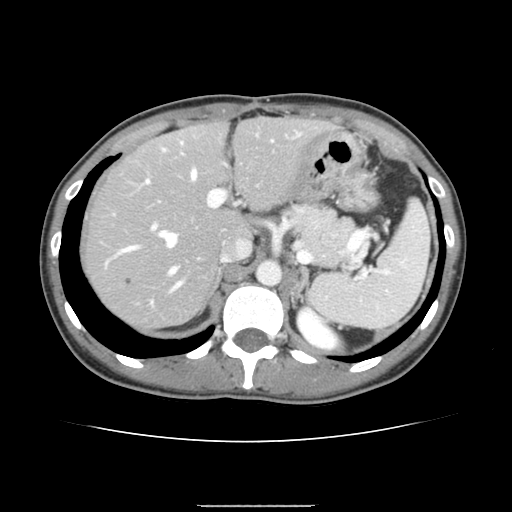
Contrast-enhanced abdominal CT, one axial slice; position 103 of 150 along the scan axis; intravenous contrast given; soft-tissue window (W 400 / L 40 HU); 2.5 mm slice thickness; 512 × 512 image matrix, field of view 324 × 324 mm. Female patient, age 32 years. Case-level facts recorded for this patient, not image findings: diagnosis: colorectal cancer liver metastases, imaged before liver resection; multiple liver metastases: yes; largest metastasis: 0.7 cm; disease in both lobes: no.
Outlined on this slice (outlined manually by an expert reader):
- hepatic veins: bounding box <122,170,197,273> (left, top, right, bottom; pixels)
- liver: <85,118,328,330>
- planned liver remnant (the part of the liver to remain after resection): <85,118,325,281>
- portal vein (with intrahepatic branches): <145,132,300,292>
- liver metastasis: <126,278,132,286>